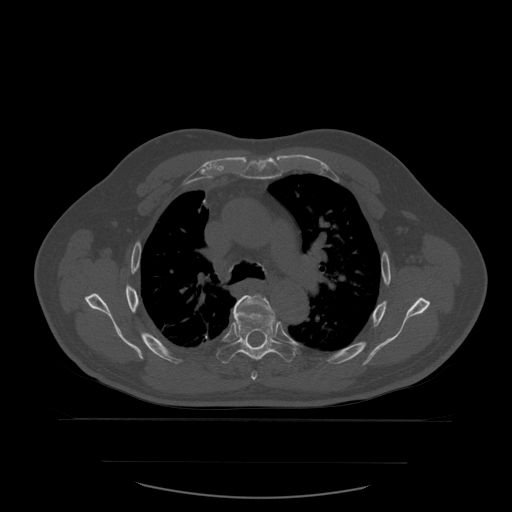
CT including the spine, one axial slice; position 410 of 590 along the scan axis; bone window (W 1800 / L 400 HU); 1.25 mm slice thickness; 512 × 512 image matrix. Patient age 71 years. Case-level facts recorded for this patient, not image findings: primary cancer: lung; vertebrae with lytic lesions (as recorded): T1, T2, L5, S1.
Outlined on this slice (semi-automatically segmented with operator editing):
- T5 vertebra: bounding box (x1, y1, x2, y2) in pixels: (235, 294, 275, 381)
- T6 vertebra: (217, 296, 295, 364)